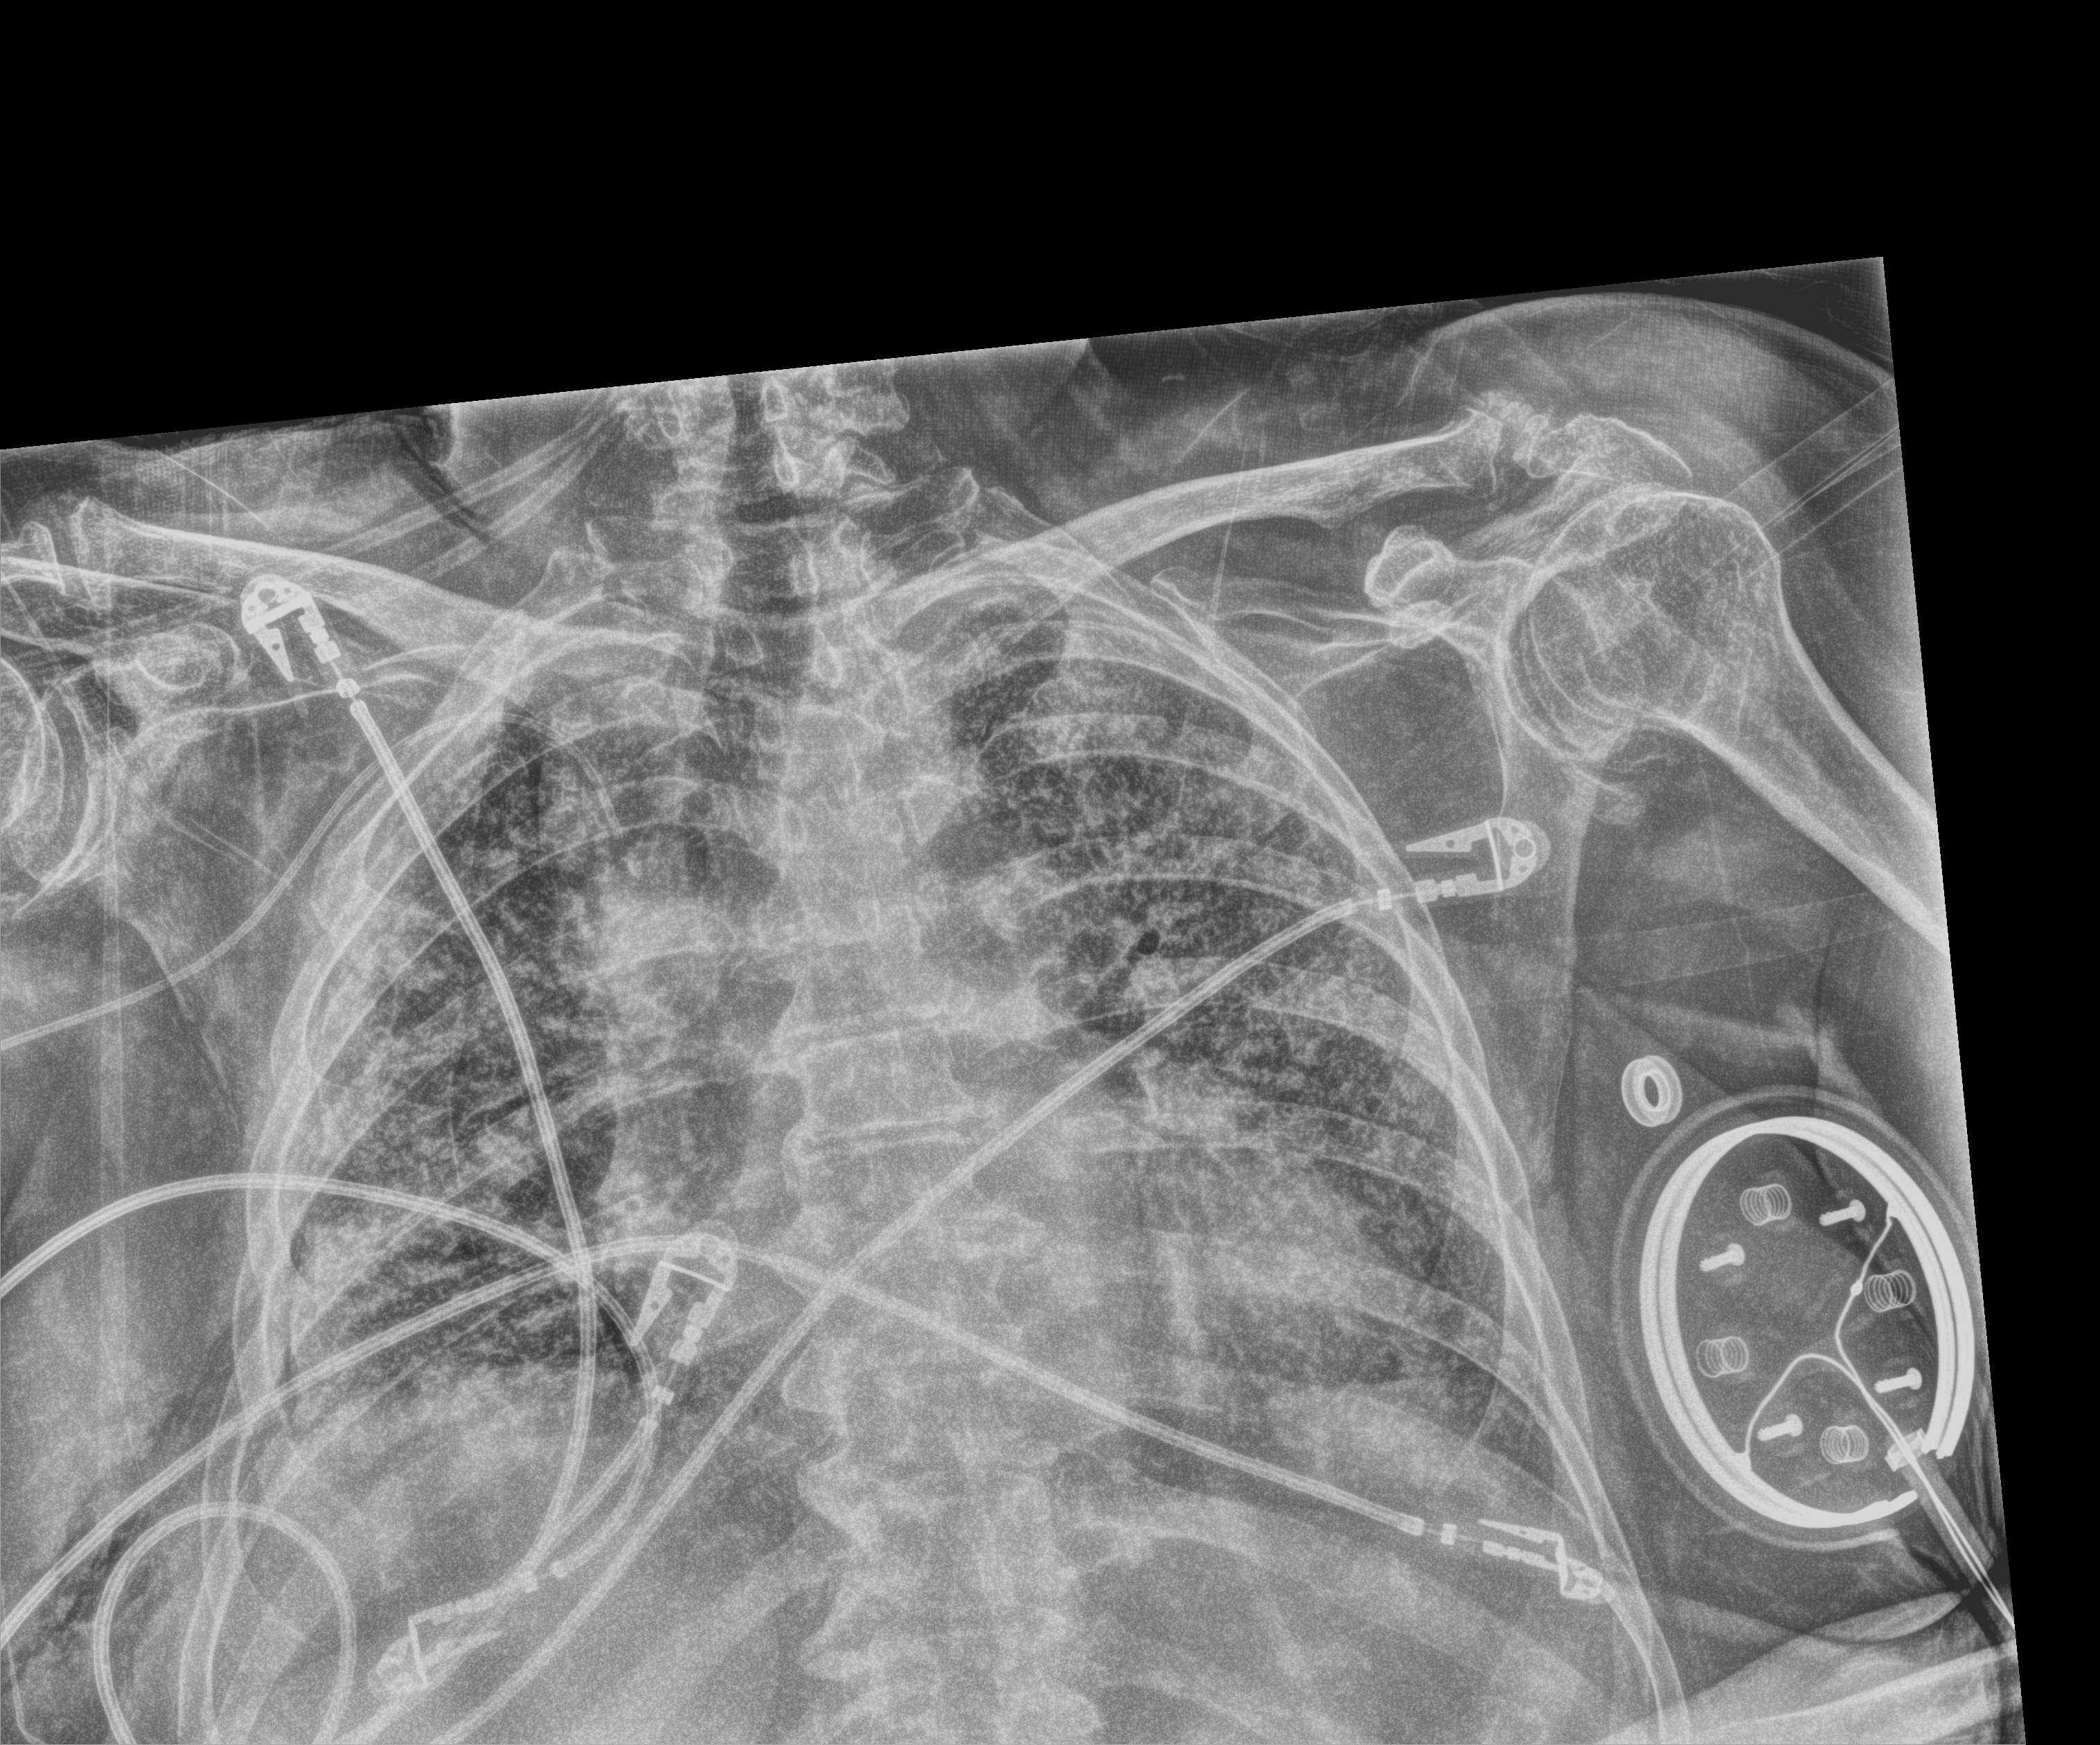
Chest X-ray (portable); anteroposterior (AP) projection. Female patient hospitalised with COVID-19, age 75–90 years.
From the hospital-stay record, not from the radiograph (when in the stay this image was taken is not recorded): mechanically ventilated during this hospital stay: yes; length of hospital stay: 56 days.